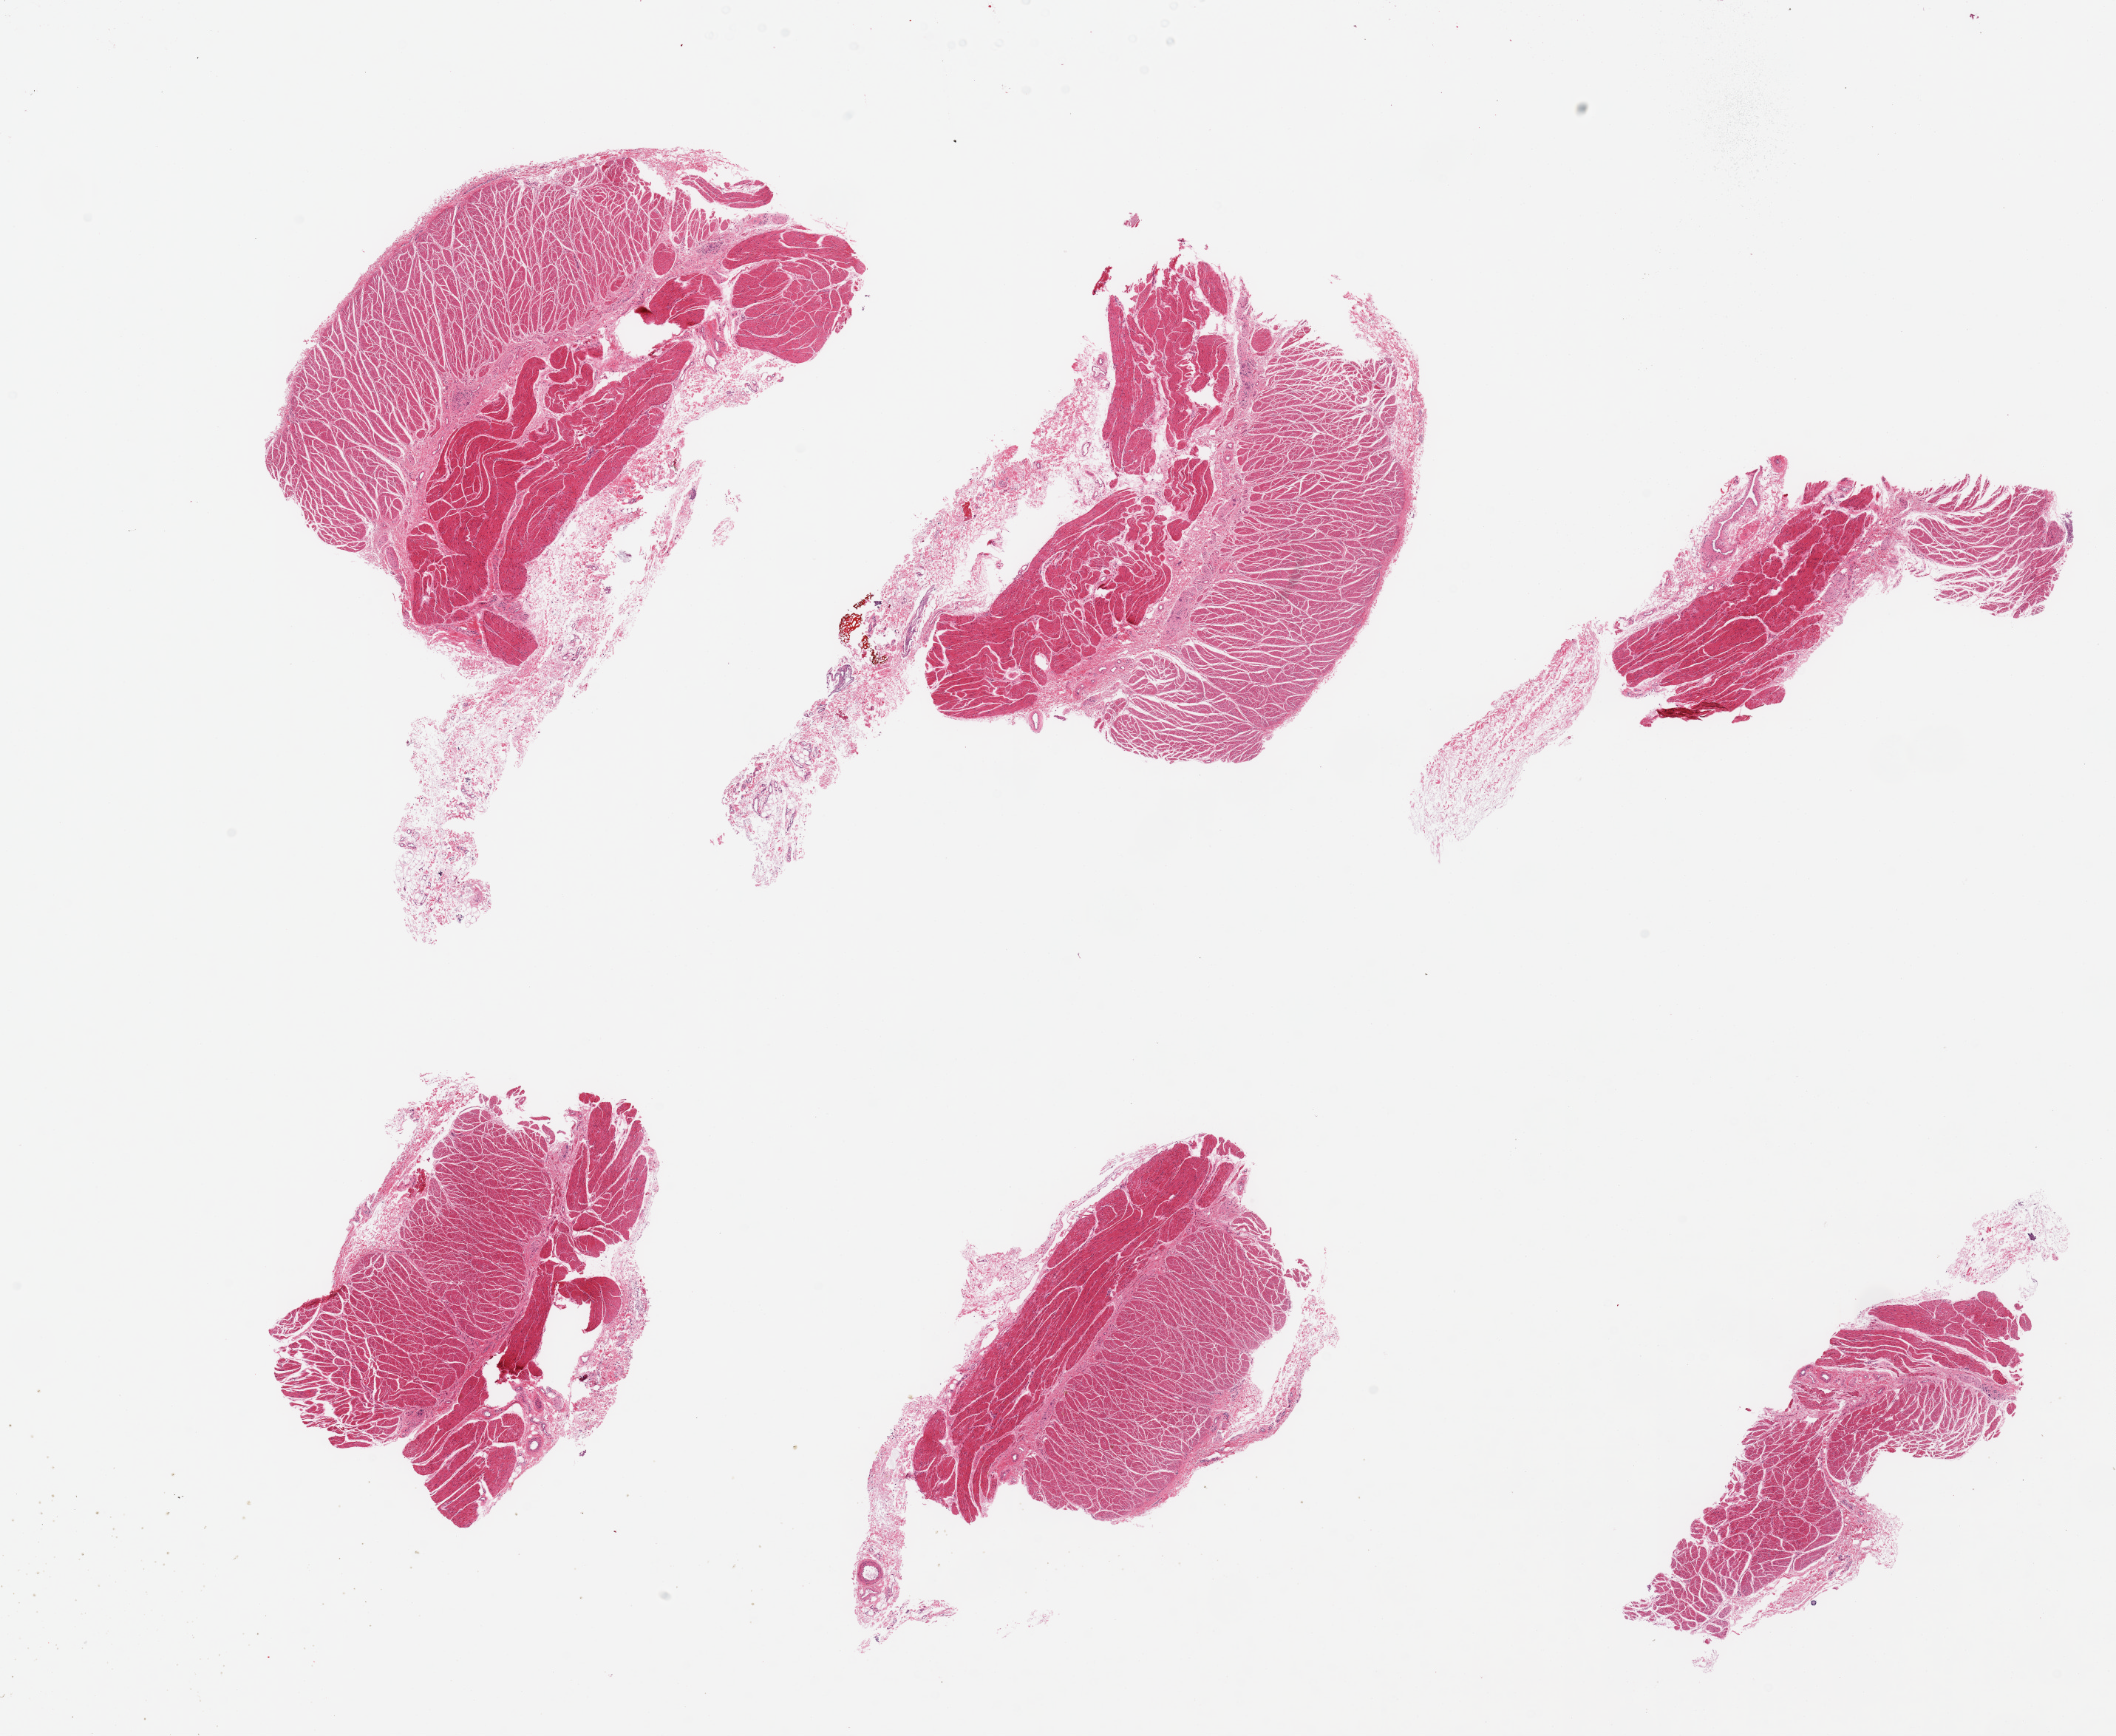
Digitized hematoxylin and eosin (H&E)-stained section — whole scanned area (about 22.6 x 18.6 mm) shown as a low-resolution overview. PAXgene-fixed paraffin-embedded (PFPE) section. Section of gastroesophageal junction (target tissue). Donor tissue sample. Male donor.
* review note (as recorded): 6 pieces; target muscularis